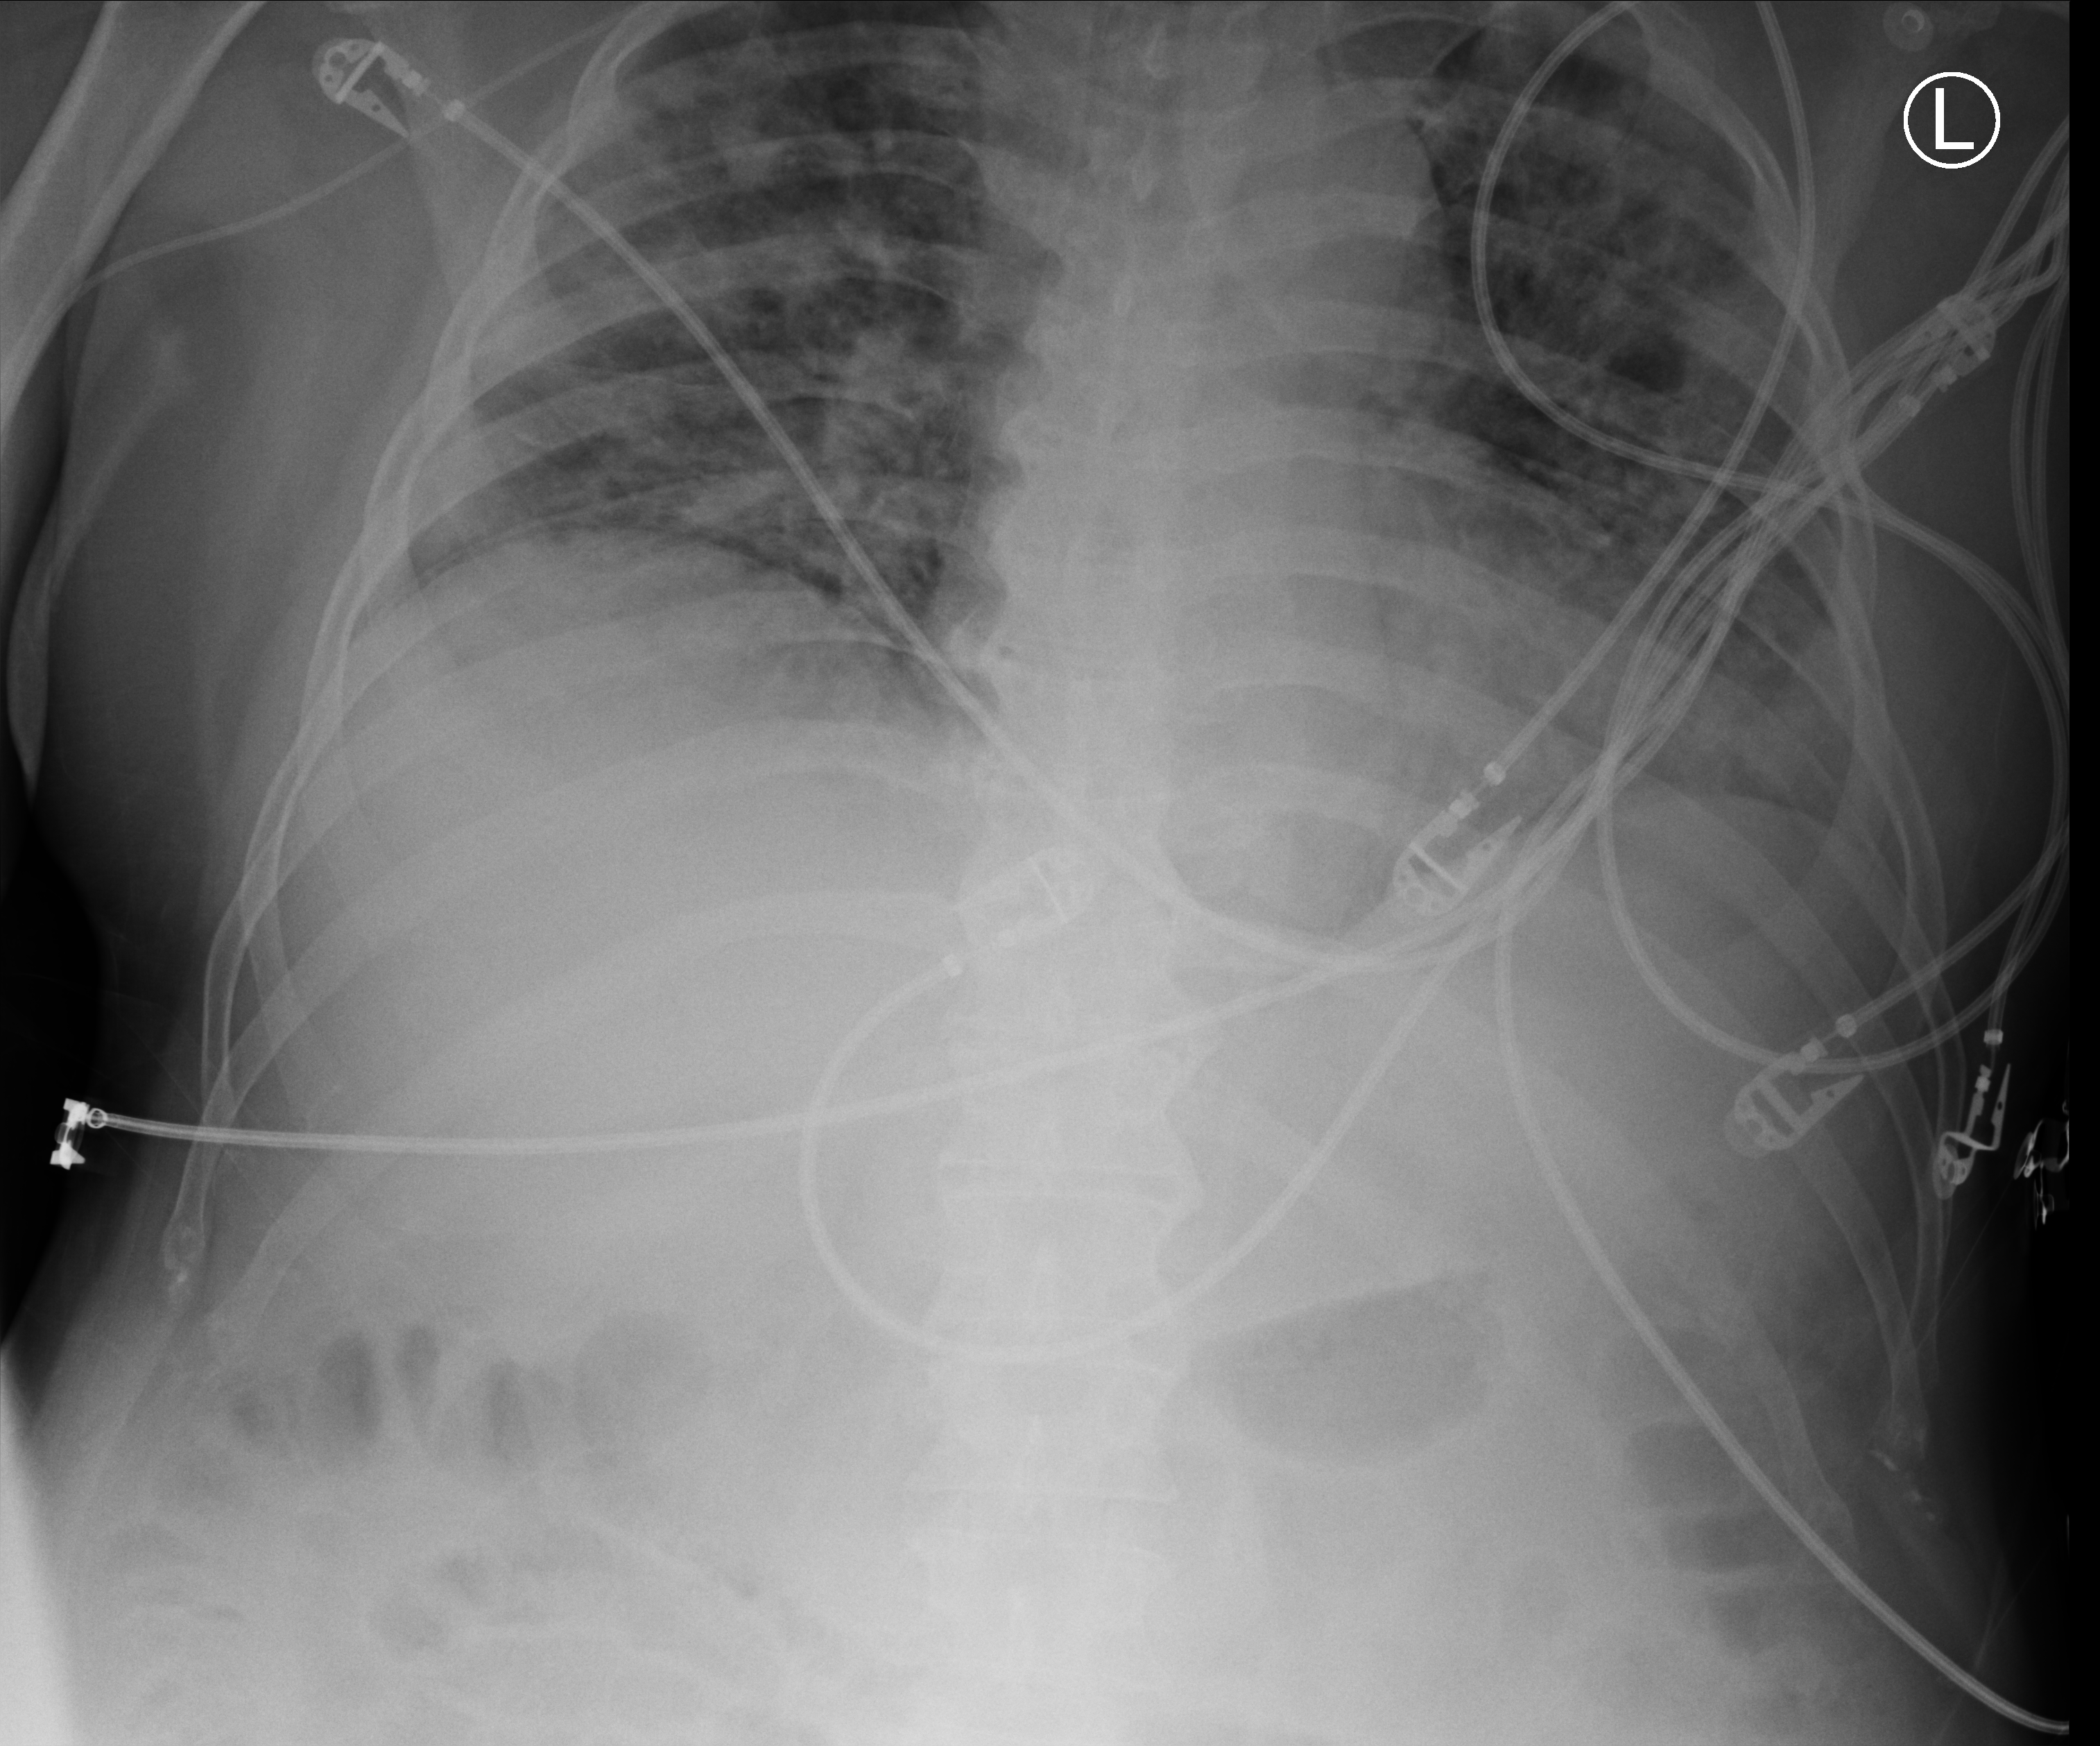
Chest X-ray (portable); anteroposterior (AP) projection. Male patient hospitalised with COVID-19, age 18–59 years.
Admission-level facts for this patient (not findings on this image; timing relative to this image not recorded): smoking status (admission record): never; admitted to intensive care during this hospital stay: yes; mechanically ventilated during this hospital stay: yes.